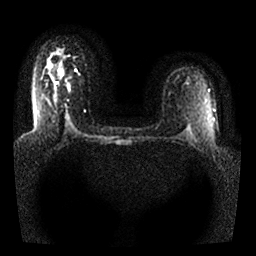
Breast MRI, one axial slice; slice 18 of 25 in the series (ordered by position); diffusion-weighted series; image 2 of 4 stored at this slice position (different b-values; order by instance number); 1.5 T; 256 × 256 image matrix, field of view 330 × 330 mm. Female patient.
Outlined on this slice (outlined manually by an expert reader):
- tumour on diffusion-weighted imaging: bounding box <65,79,67,83> (left, top, right, bottom; pixels)